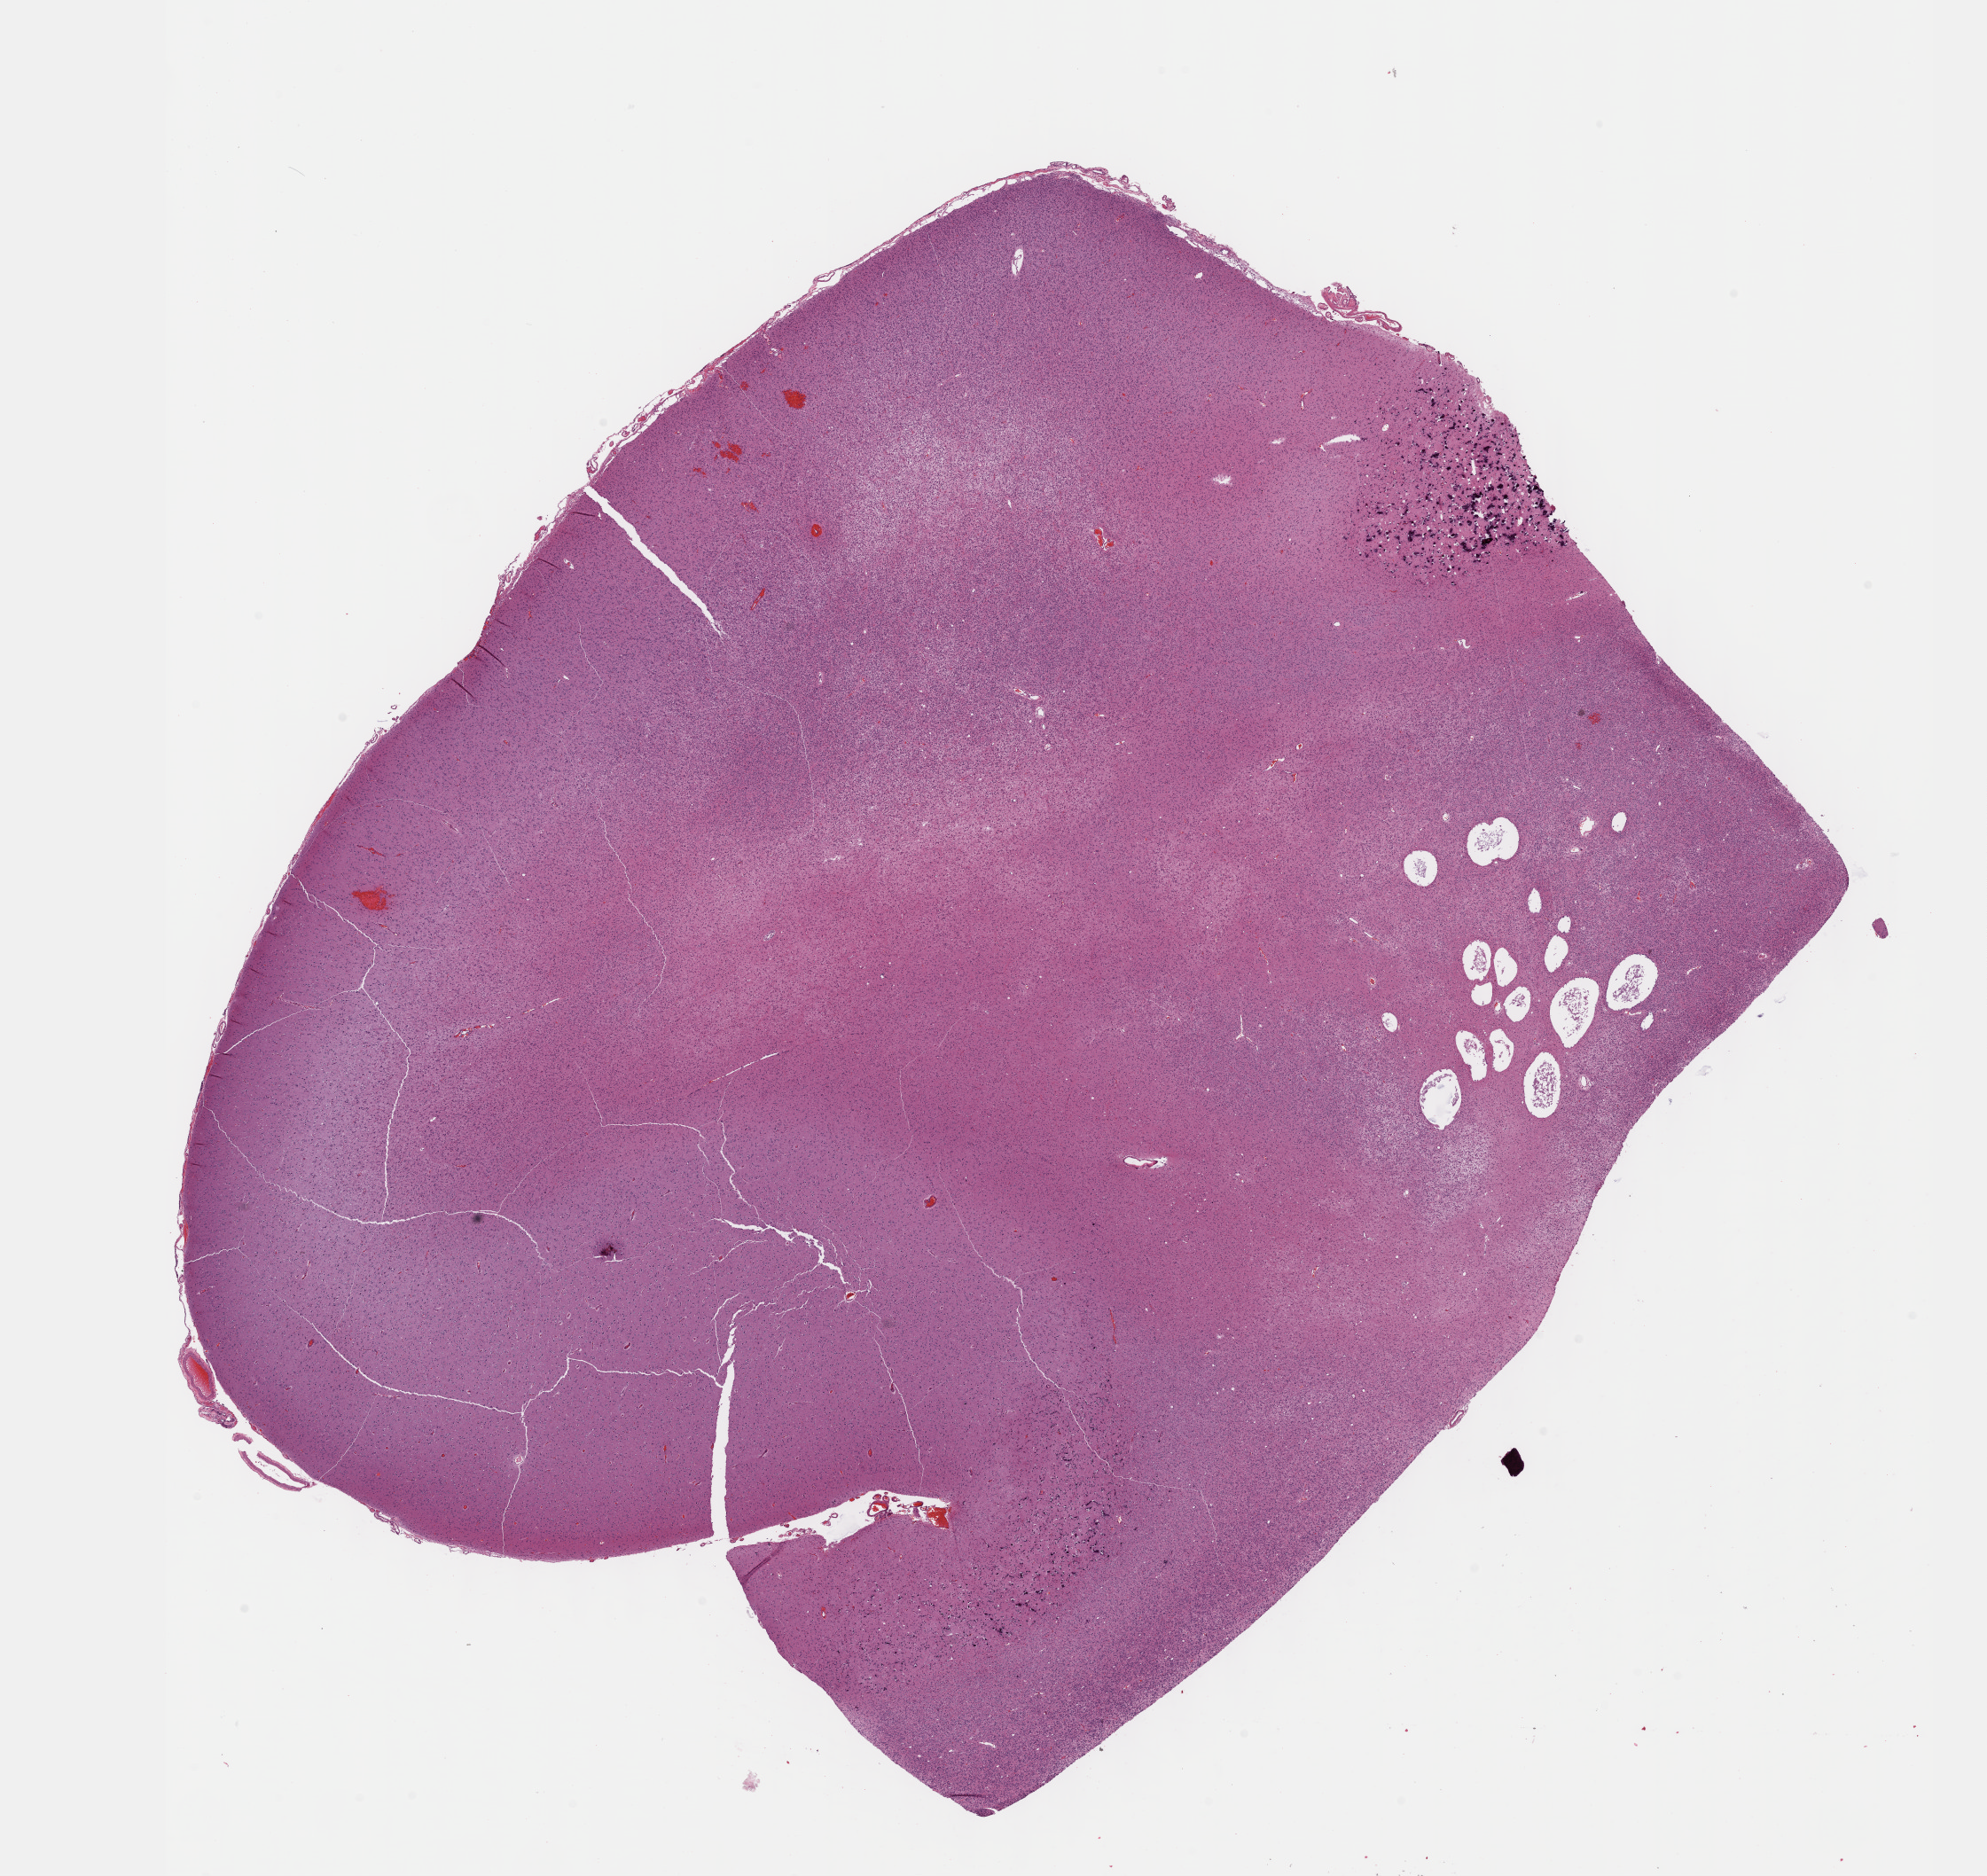
Whole-slide histology image, H&E-stained, low-resolution overview of the scanned area, about 18.1 x 17.1 mm (slide scanned at 40x), FFPE section, primary tumour sample from the brain. Patient: female, age at initial diagnosis 41 years. Histologic grade: G3 (poorly differentiated).
Histologic diagnosis: Oligodendroglioma, anaplastic. Laterality: right.